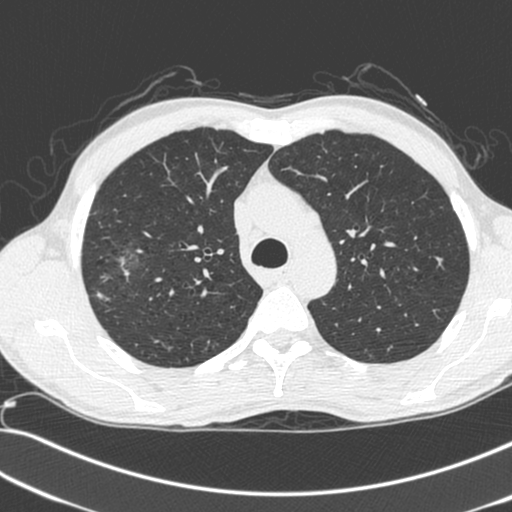
Chest CT (low-dose screening protocol), one axial image, baseline screening round, lung window (W 1500 / L -600 HU), standard (soft-tissue) reconstruction kernel (C), slice 69 of 281 in the series. Male participant, aged 55 years at enrolment. Current smoker at enrolment.
- Expert reader's lesion annotation, bounding box <72,238,150,310> (left, top, right, bottom; pixels).
- The exam's reader record, not a measurement of the box and not confirmed to be the same lesion: non-calcified nodule or mass ≥4 mm, right upper lobe, 52 × 39 mm, spiculated (stellate) margins, soft tissue attenuation.
- Official screen result: positive, change unspecified: nodule(s) >= 4 mm or enlarging nodule(s), mass(es), or other non-specific abnormalities suspicious for lung cancer.
- Lung cancer was diagnosed 25 days after this screen: large cell neuroendocrine carcinoma, right upper lobe, poorly differentiated (G3), stage IIB (AJCC 6th edition), 49 mm at pathology.